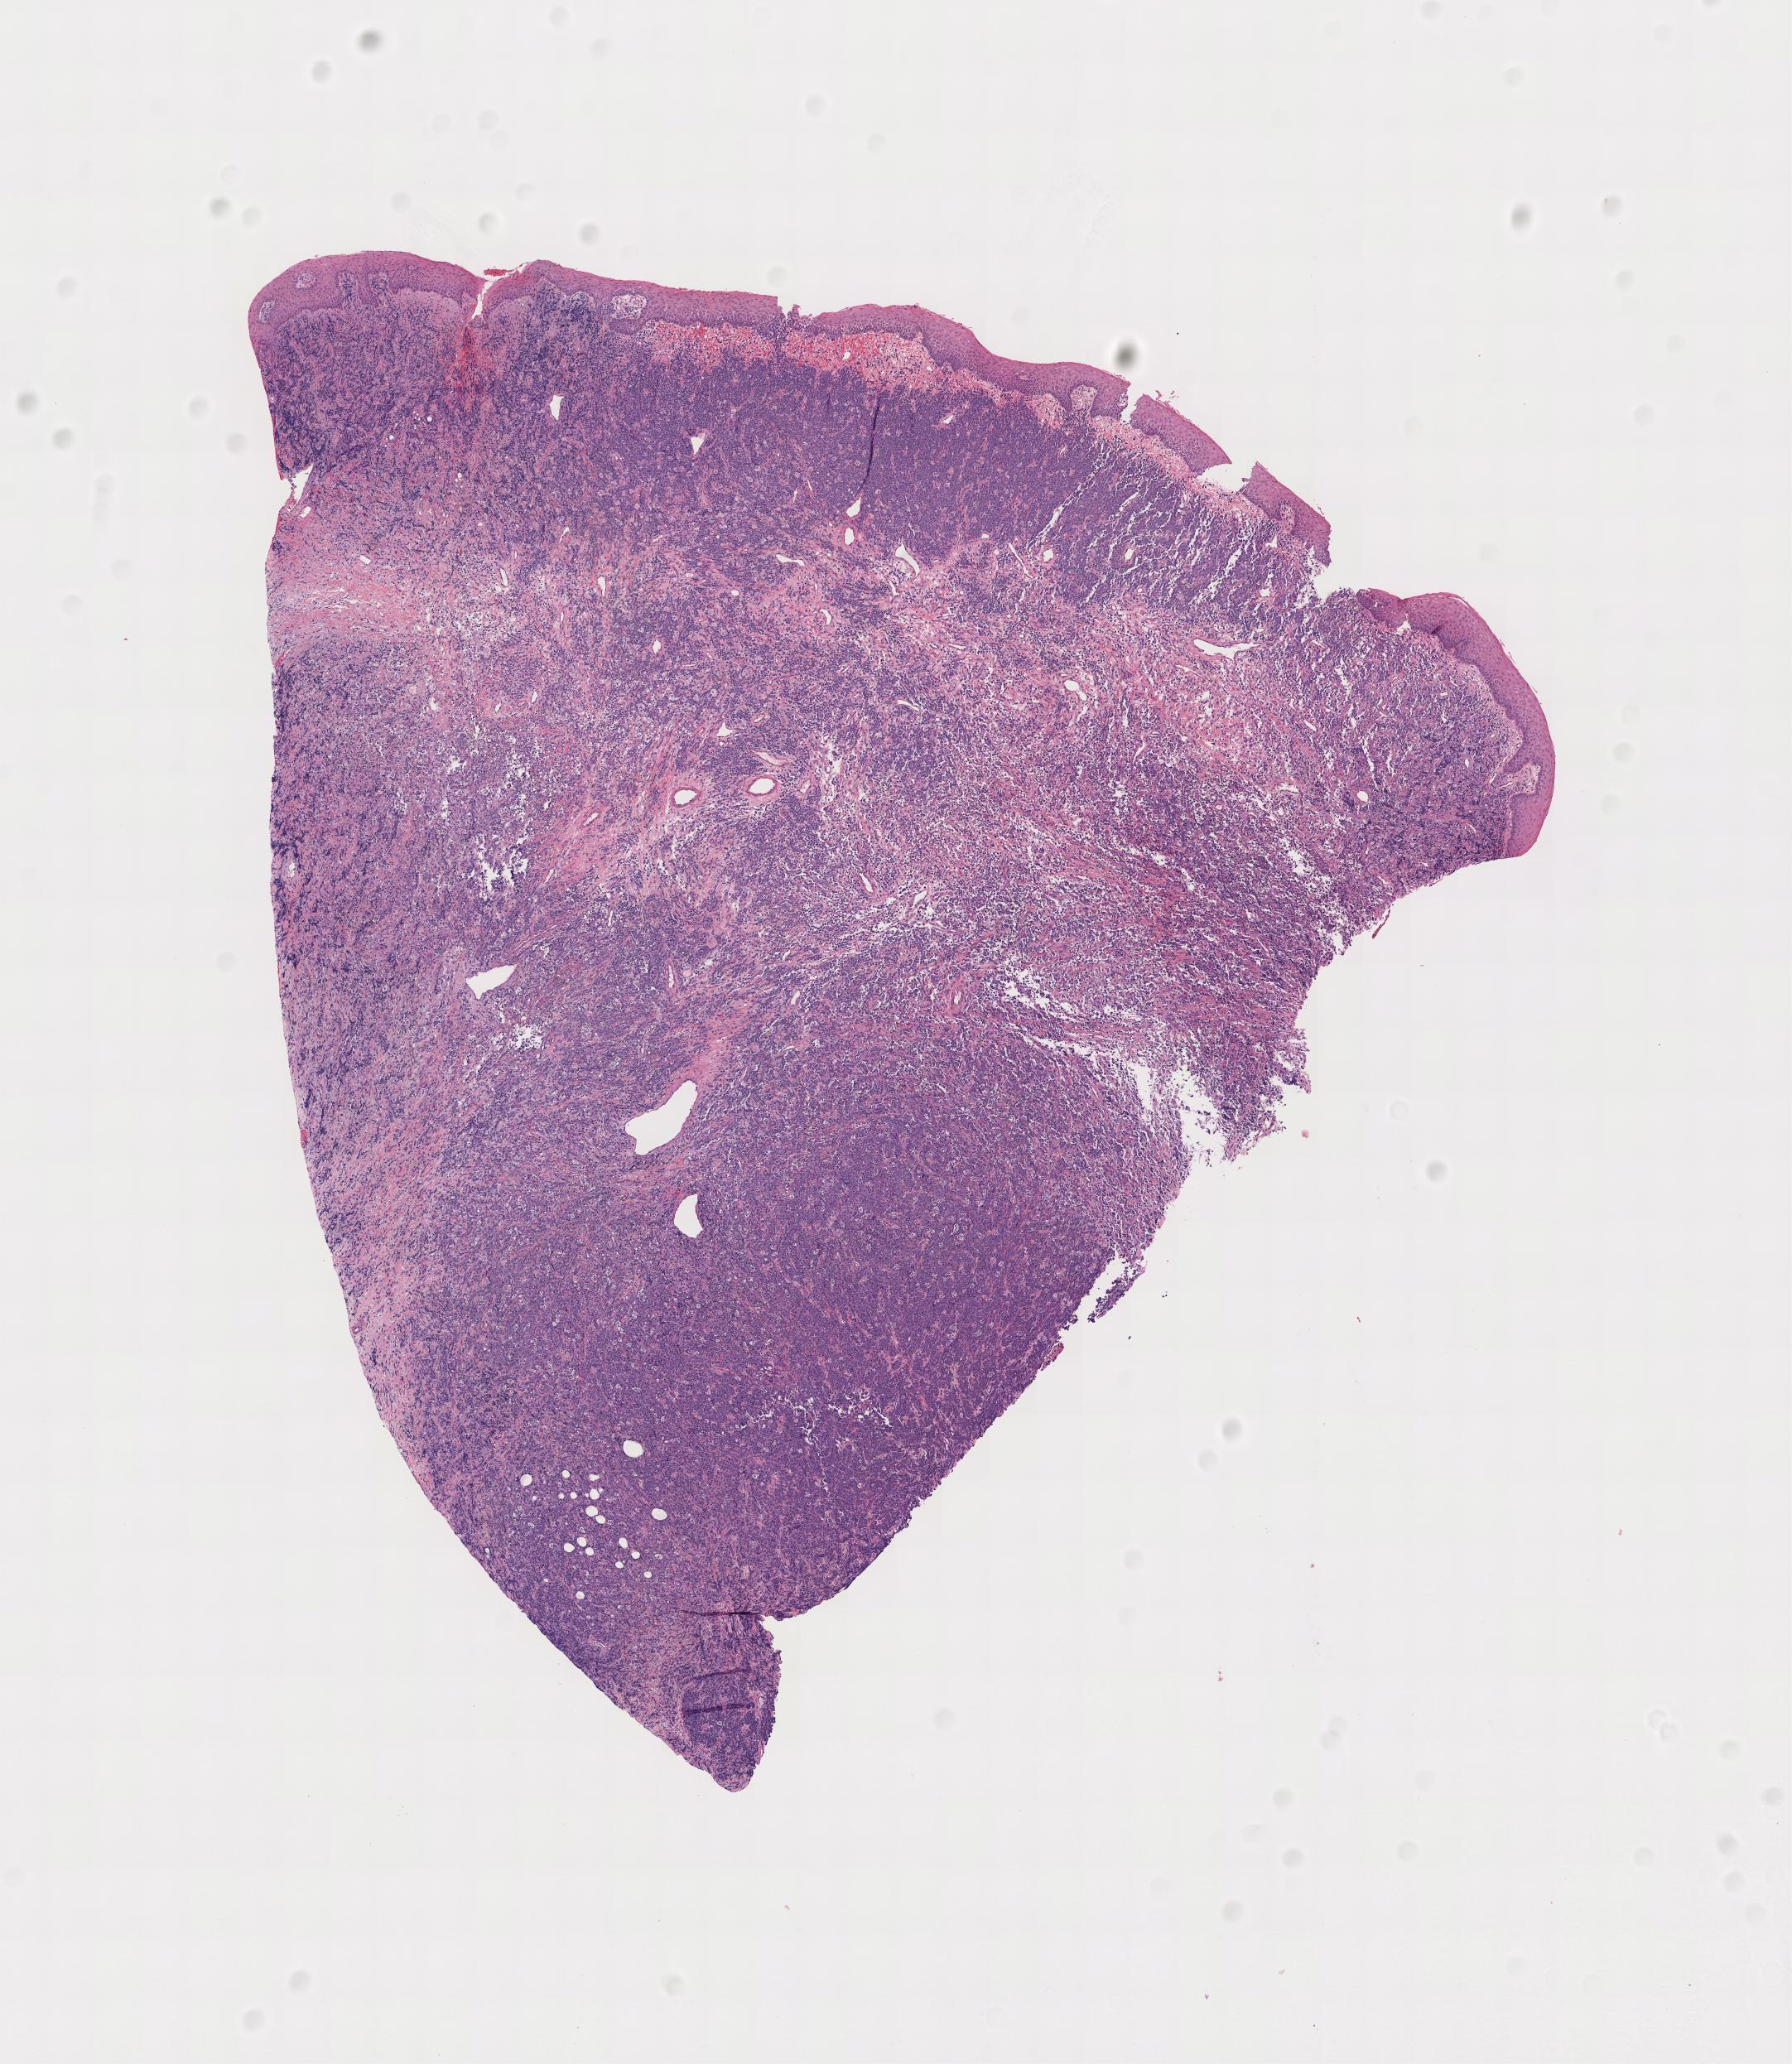
Whole-slide image, haematoxylin and eosin stain, low-resolution overview of the scanned area; tumor tissue; site: cranium. Patient: male, age at initial diagnosis 5 years.
Diagnosis: Diffuse large B-cell lymphoma, NOS.